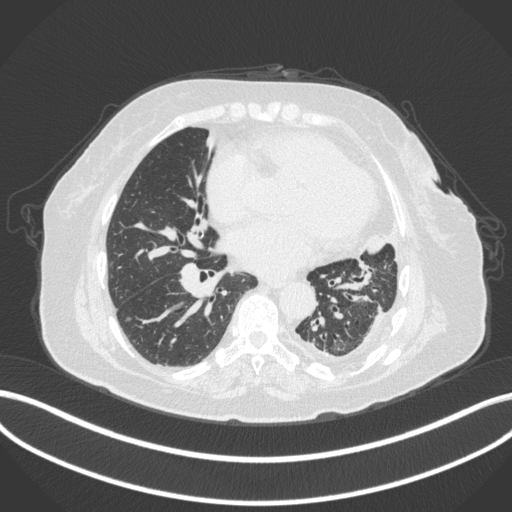
Chest CT, one axial slice; position 162 of 399 along the scan axis; reconstruction kernel B31f; 120 kVp; lung window (W 1500 / L -600 HU); 1 mm slice thickness; 512 × 512 image matrix. Patient: female, 75 years. Case-level facts recorded for this patient, not image findings: clinical TNM (as recorded): T3 N3 M1.
Outlined on this slice (bounding box drawn by a radiologist):
- lung tumour (recorded histology: adenocarcinoma): bounding box <363,230,388,260> (left, top, right, bottom; pixels)